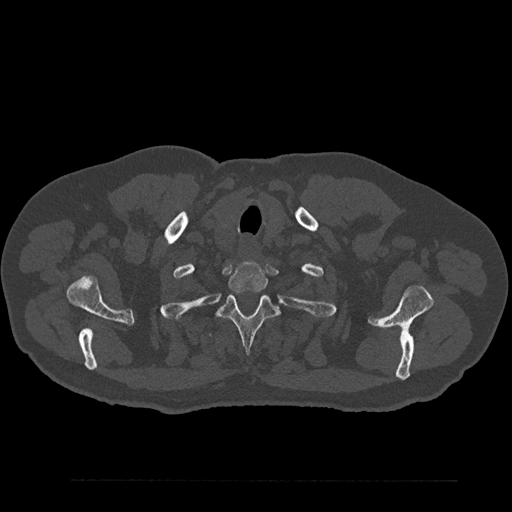
CT including the spine, one axial slice. Position 725 of 797 along the scan axis. 120 kVp. Bone window (W 1800 / L 400 HU). 0.5 mm slice thickness. 512 × 512 image matrix, field of view 430 × 430 mm. Male patient, age 61 years. Case-level facts recorded for this patient, not image findings: primary cancer: prostate.
Structures marked on this image (semi-automatically segmented with operator editing):
- T1 vertebra: bounding box (x1, y1, x2, y2) in pixels: (228, 262, 268, 292)
- T2 vertebra: (218, 295, 279, 353)
- T3 vertebra: (207, 332, 213, 338)